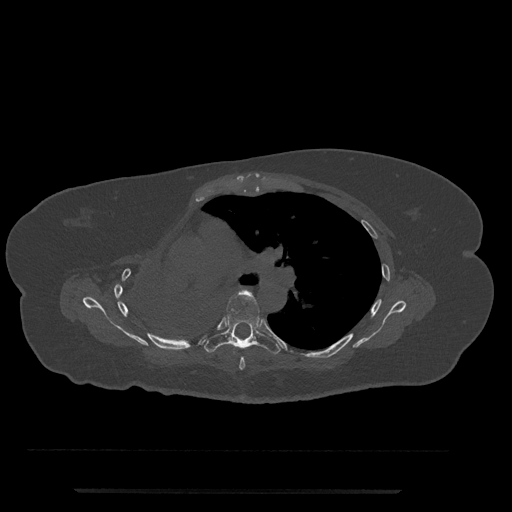
CT including the spine, one axial slice. Position 506 of 797 along the scan axis. Bone window (W 1800 / L 400 HU). 0.5 mm slice thickness. 512 × 512 image matrix, field of view 440 × 440 mm. Patient: female, 51 years. Case-level facts recorded for this patient, not image findings: primary cancer: neuro.
Outlined on this slice (semi-automatically segmented with operator editing):
- T5 vertebra: bounding box <239,320,264,370> (left, top, right, bottom; pixels)
- T6 vertebra: <206,291,280,355>